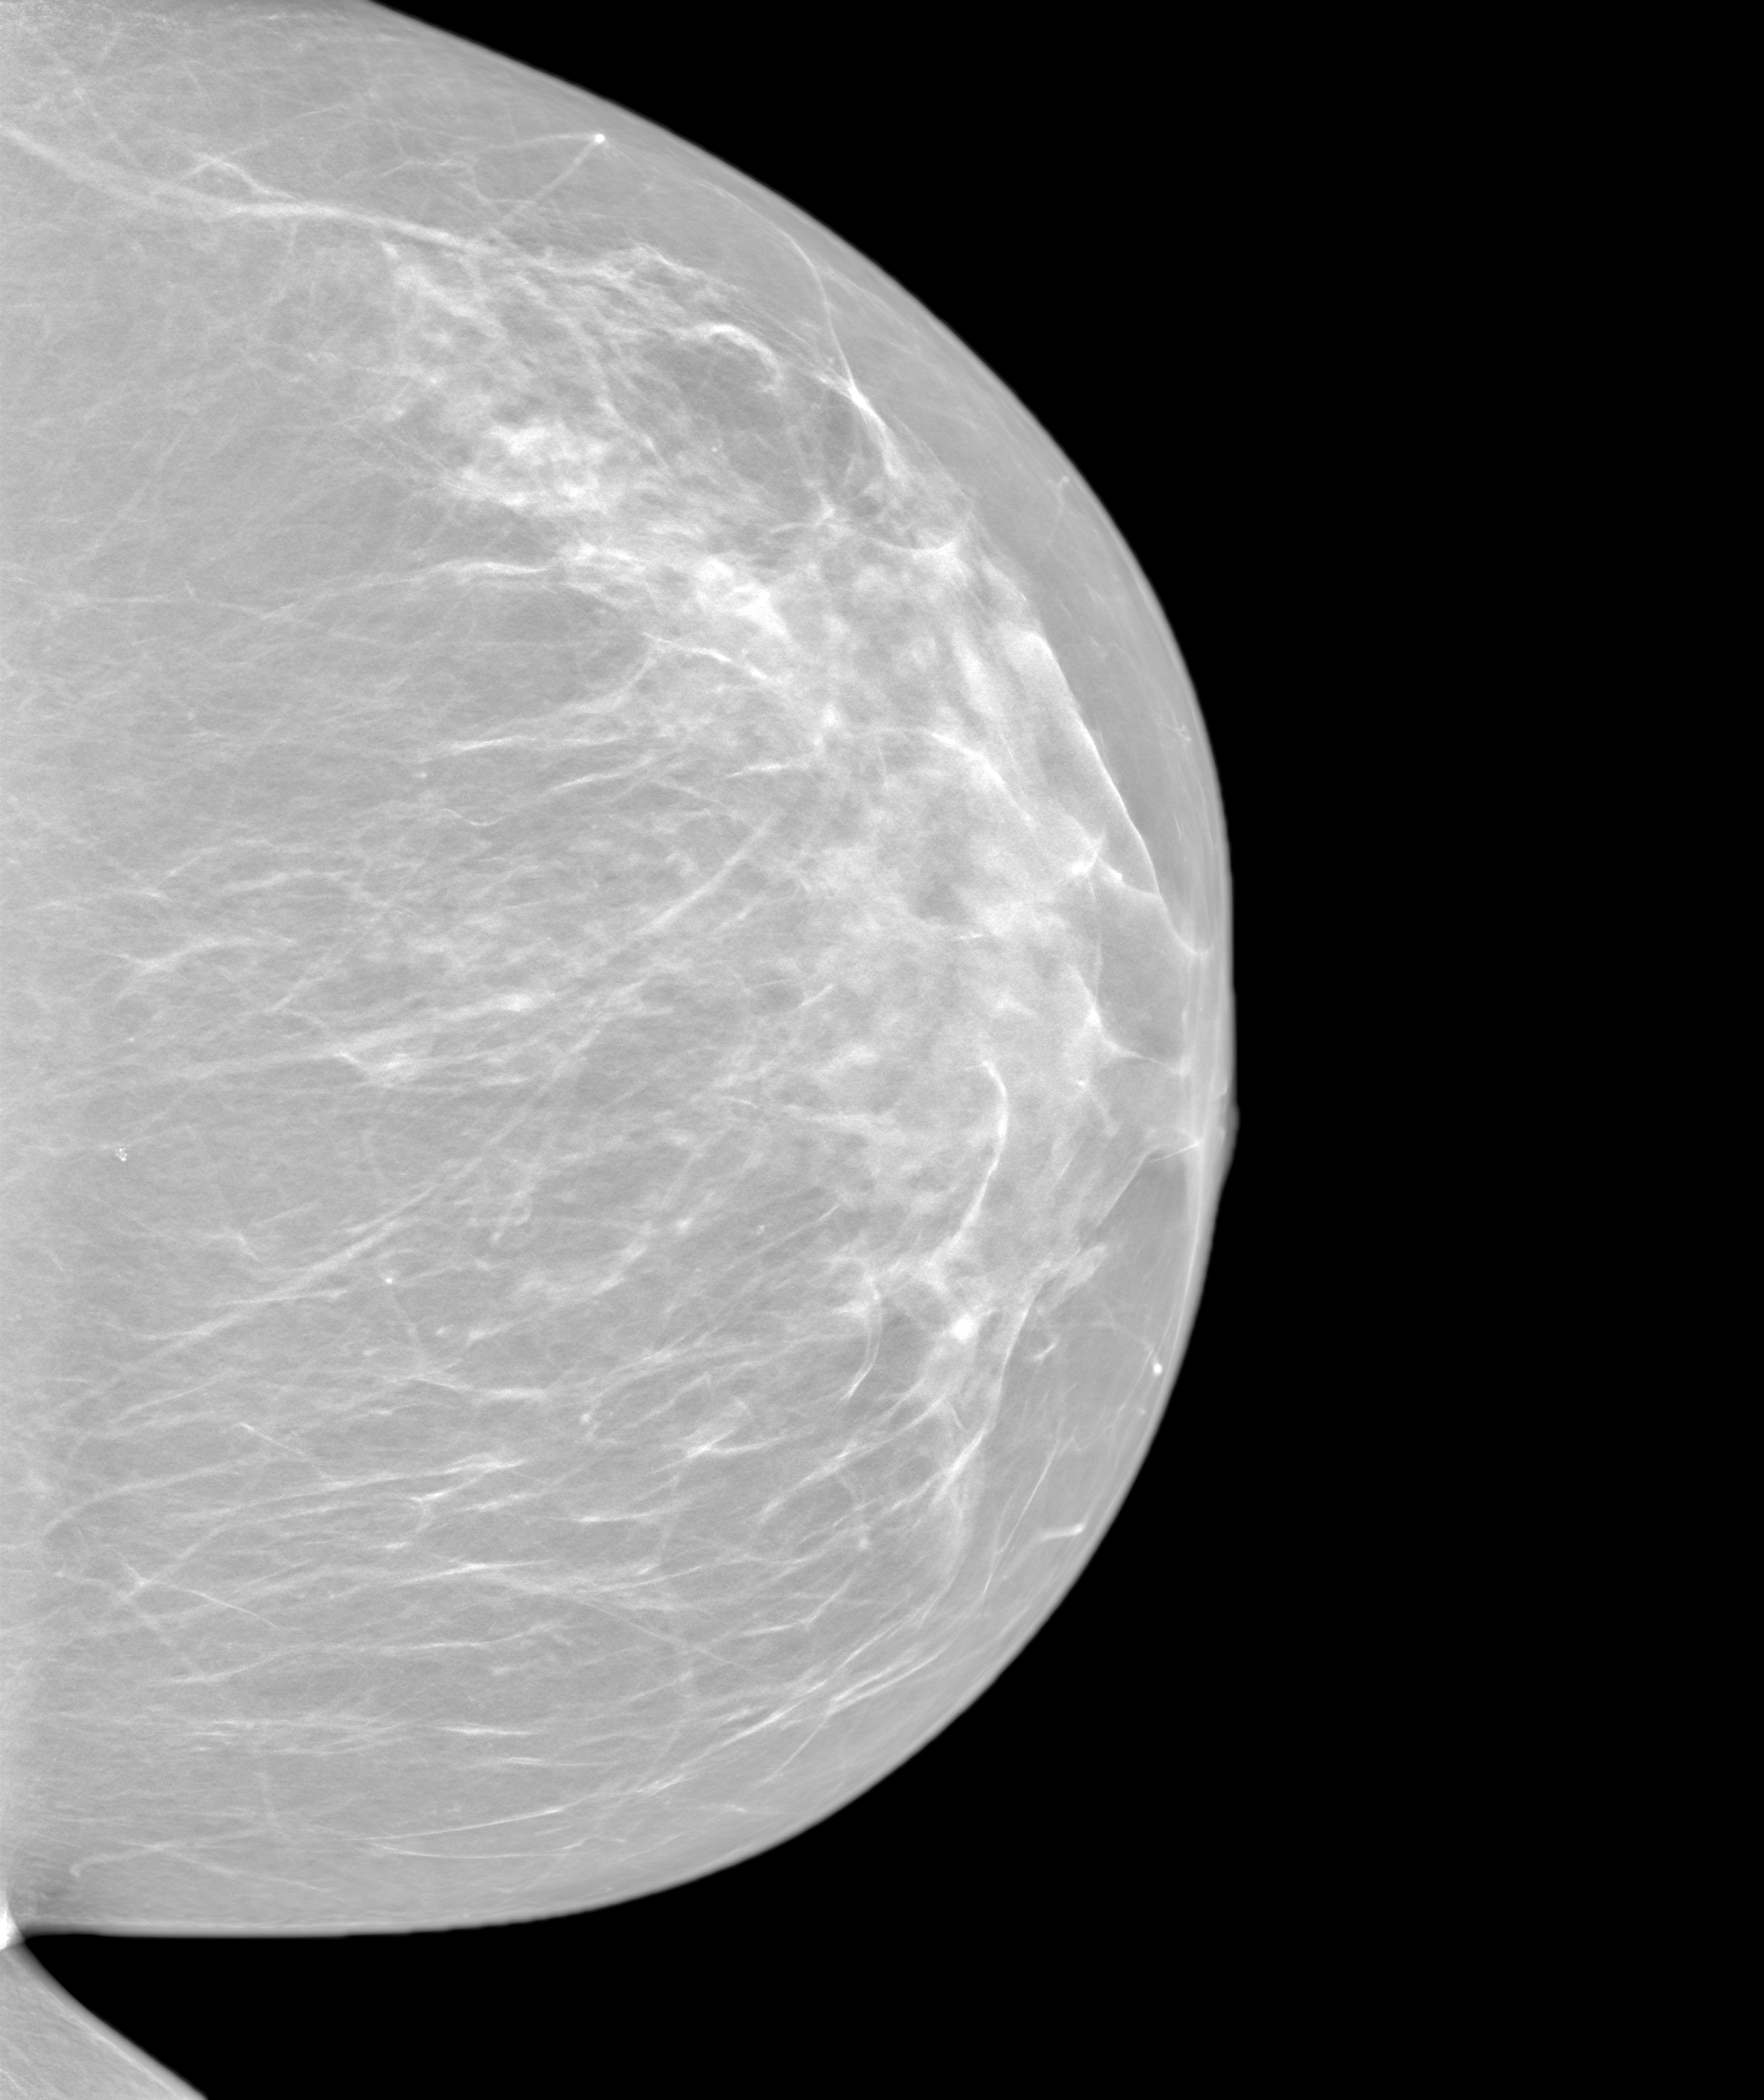
Annual screening mammography examination. Female patient, age 57 years.
Image type: synthesized 2-D view from tomosynthesis. Breast: left. Projection: CC view.